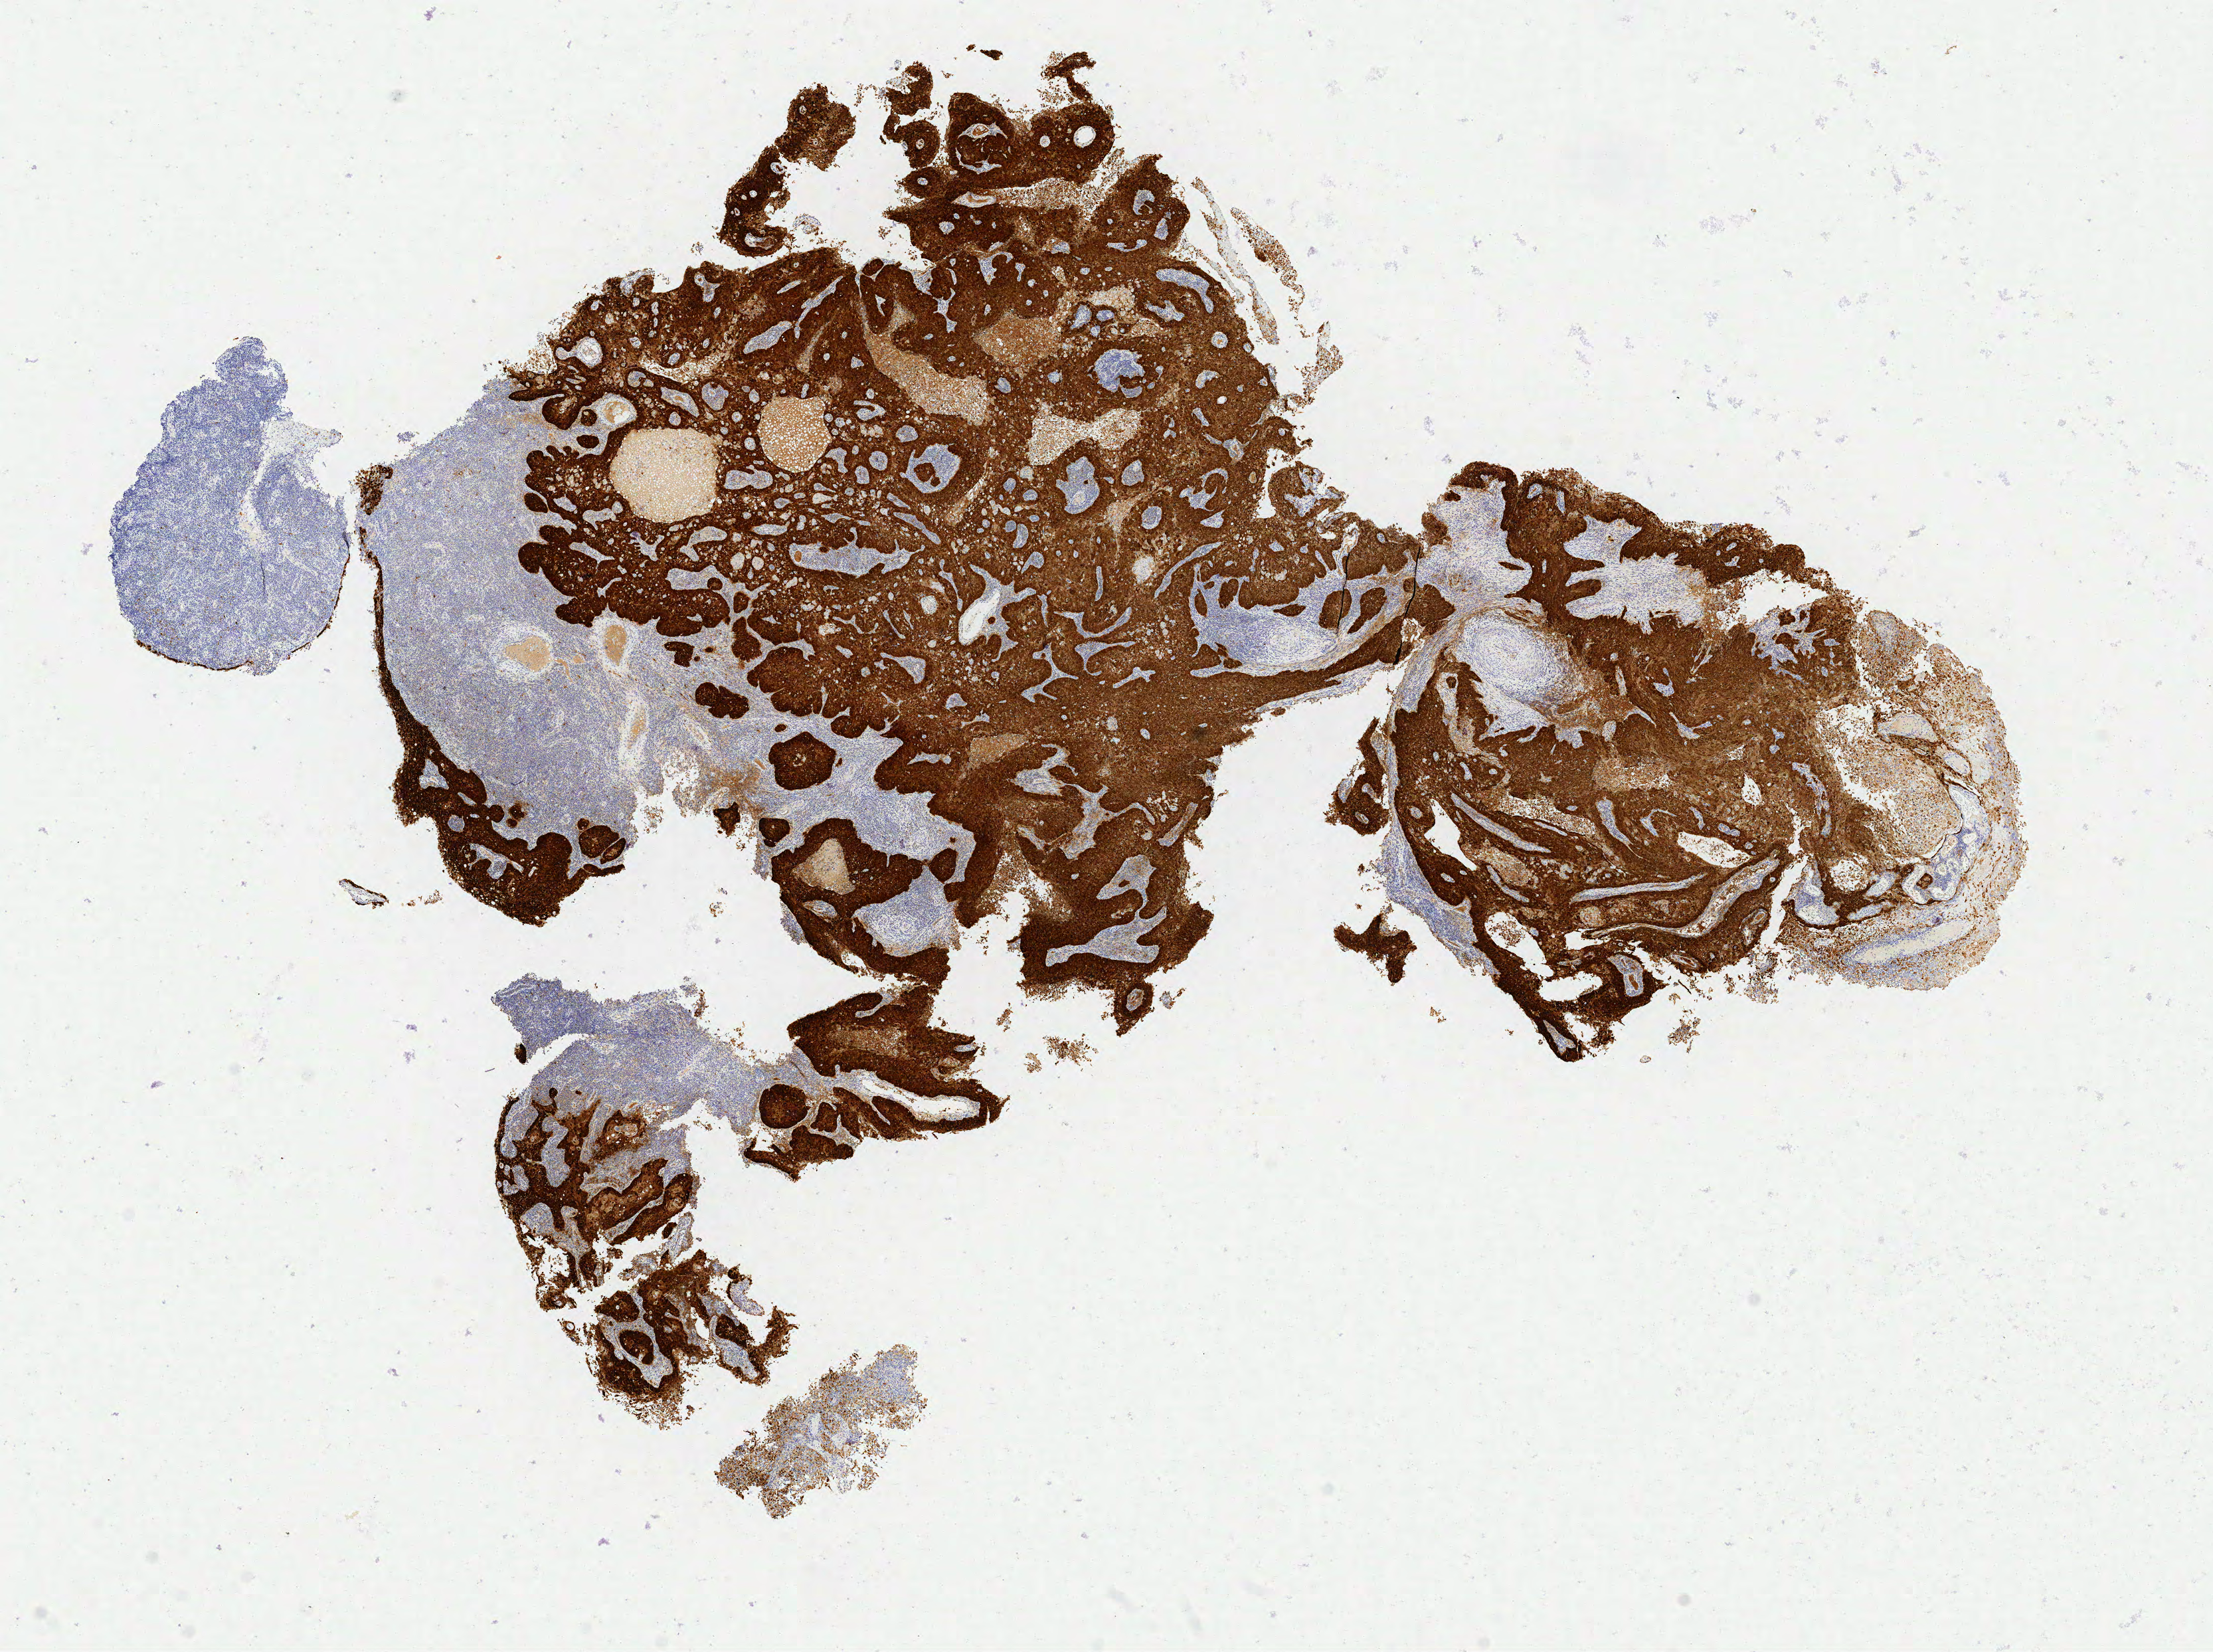
IHC for p16 (p16INK4a), whole-slide image, whole scanned area (about 13.3 x 9.9 mm) shown as a low-resolution overview. Specimen: tumor tissue. Site: cervix. Female patient, aged 34.
• histologic diagnosis: Squamous cell carcinoma, large cell, nonkeratinizing, NOS